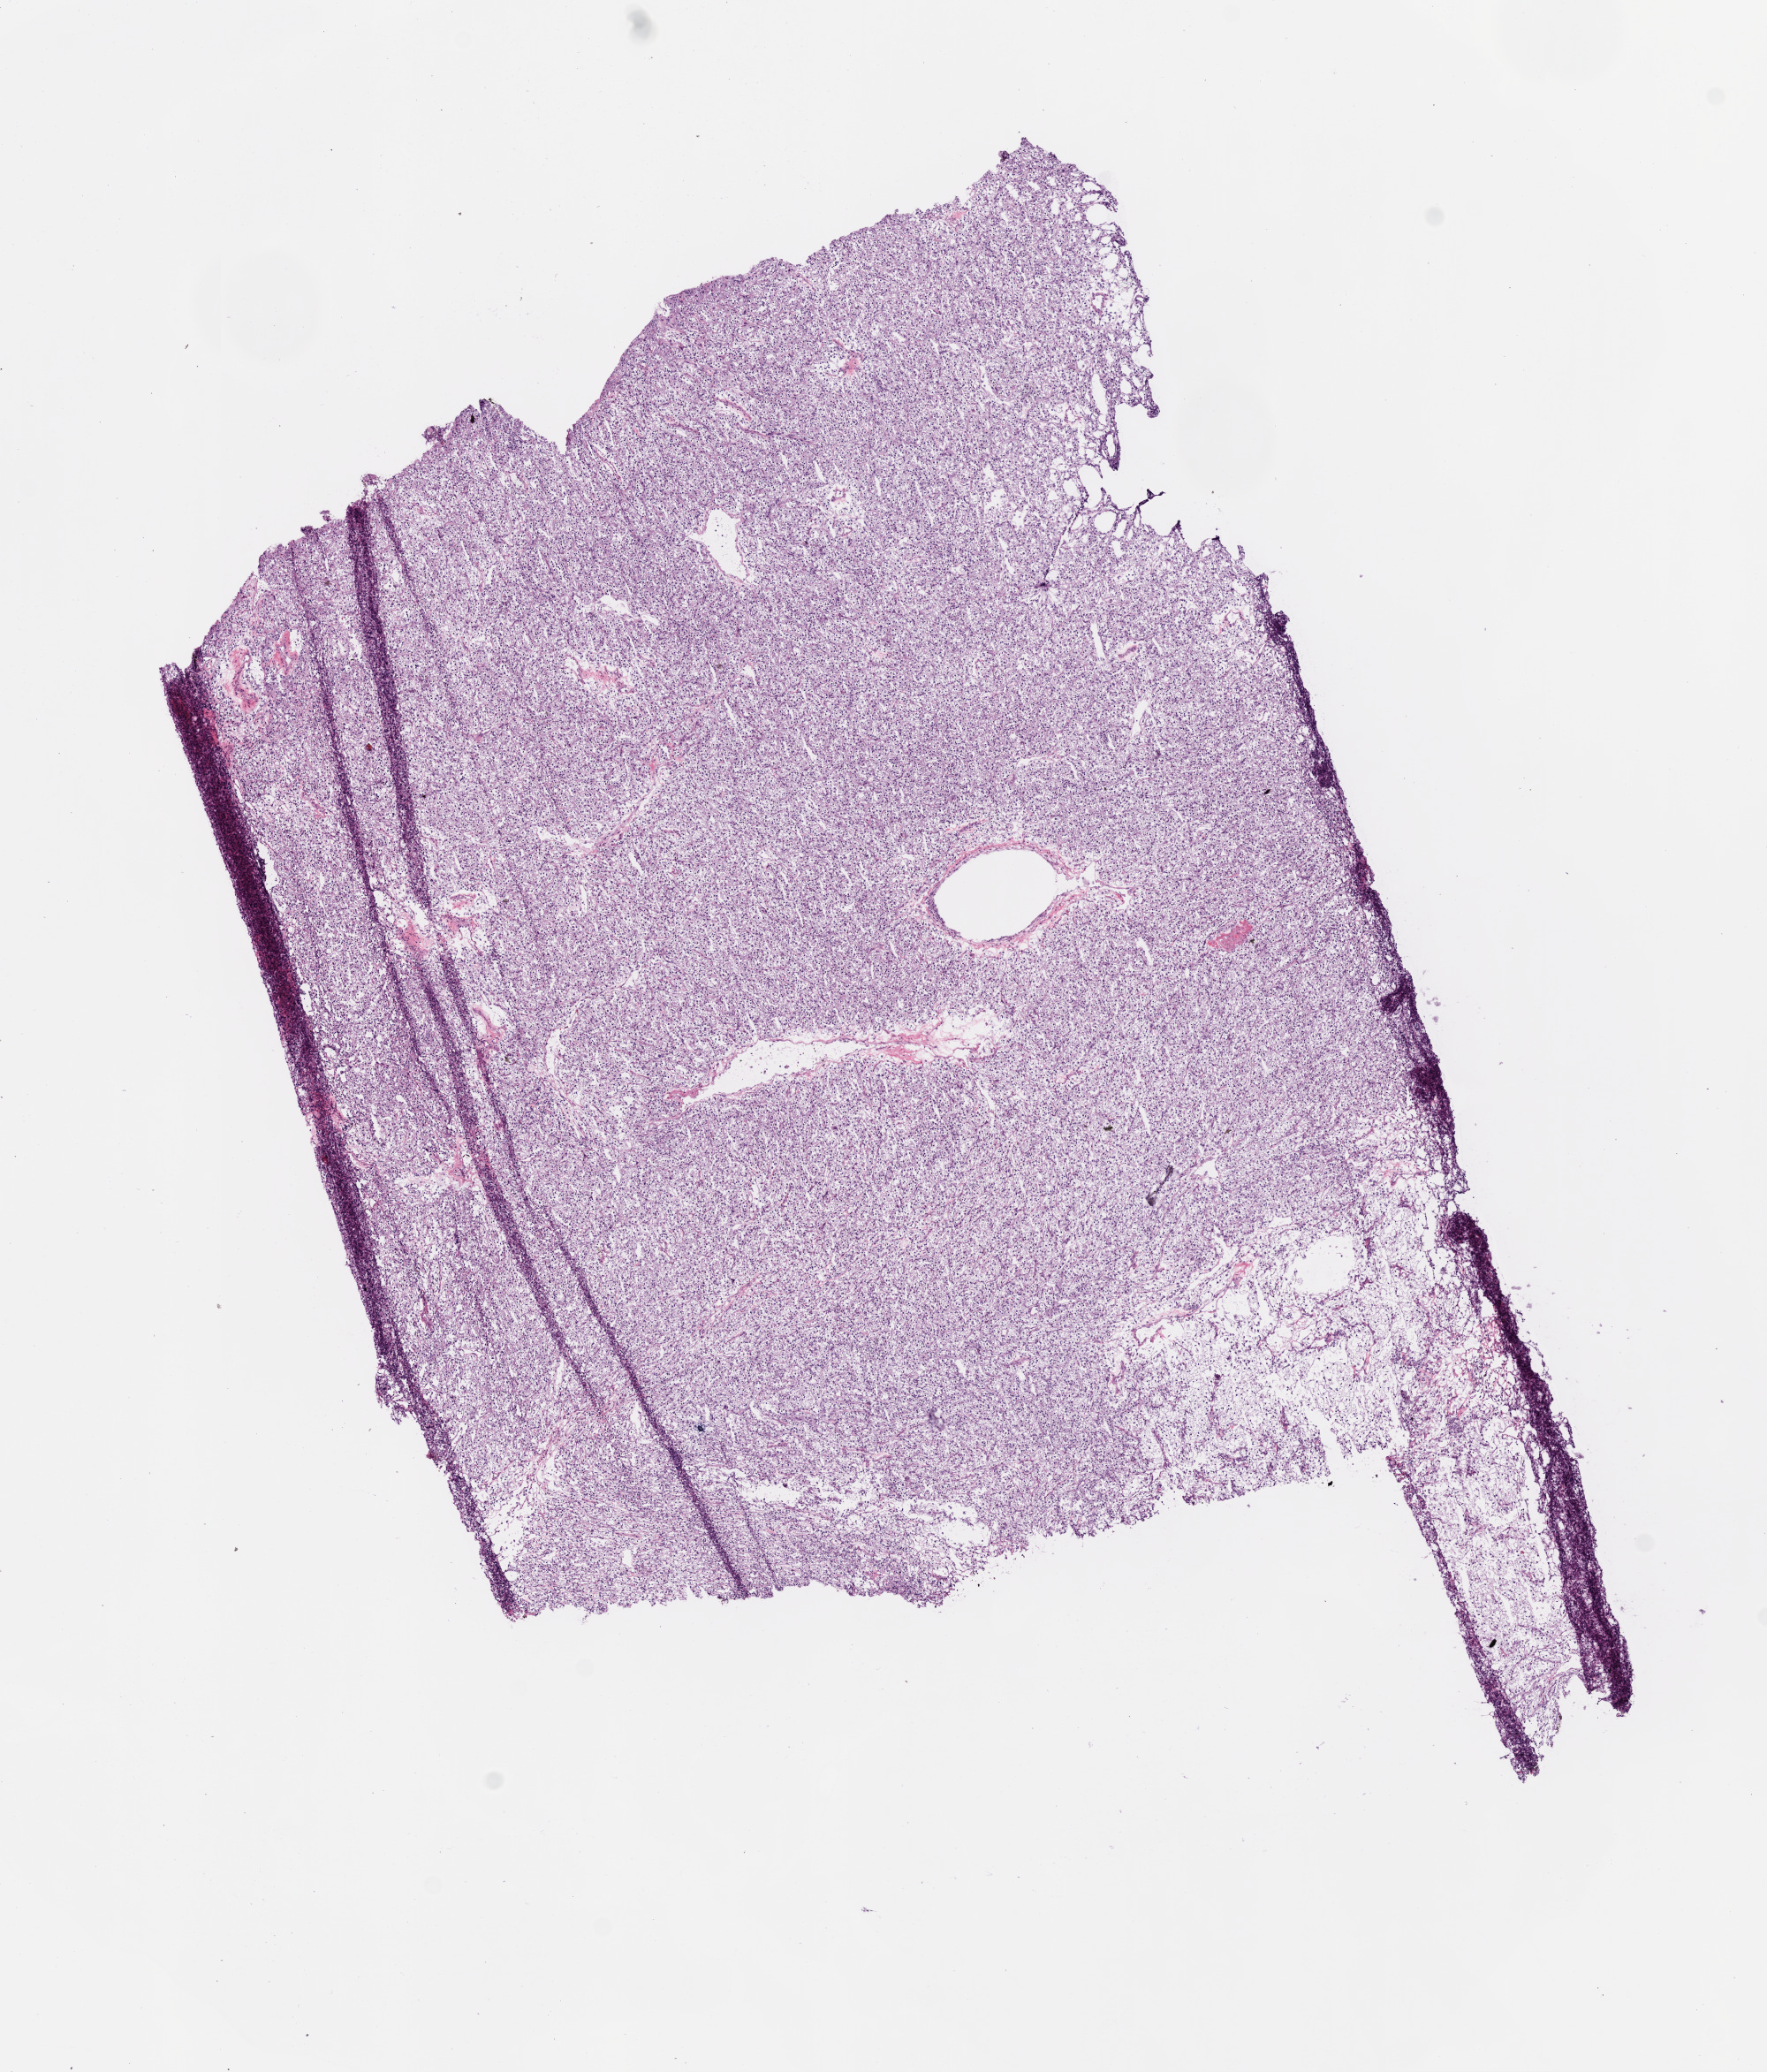
Digitized H&E tissue section (whole slide) — shown as a low-resolution overview of the whole scanned area (about 8.0 x 9.4 mm, acquisition: 20x scan). Frozen section from the top of the tissue portion. Sample: primary tumour, kidney. Male patient; age at initial diagnosis 53 years. Histologic grade: G1 (well differentiated). Composition of this section per pathologist review: tumour cells 95%, tumour nuclei 85%, normal cells 0%, stromal cells 5%, necrosis 0%.
AJCC pathologic stage: I. Pathologic diagnosis: Clear cell adenocarcinoma, NOS. TNM: T1b NX M0.